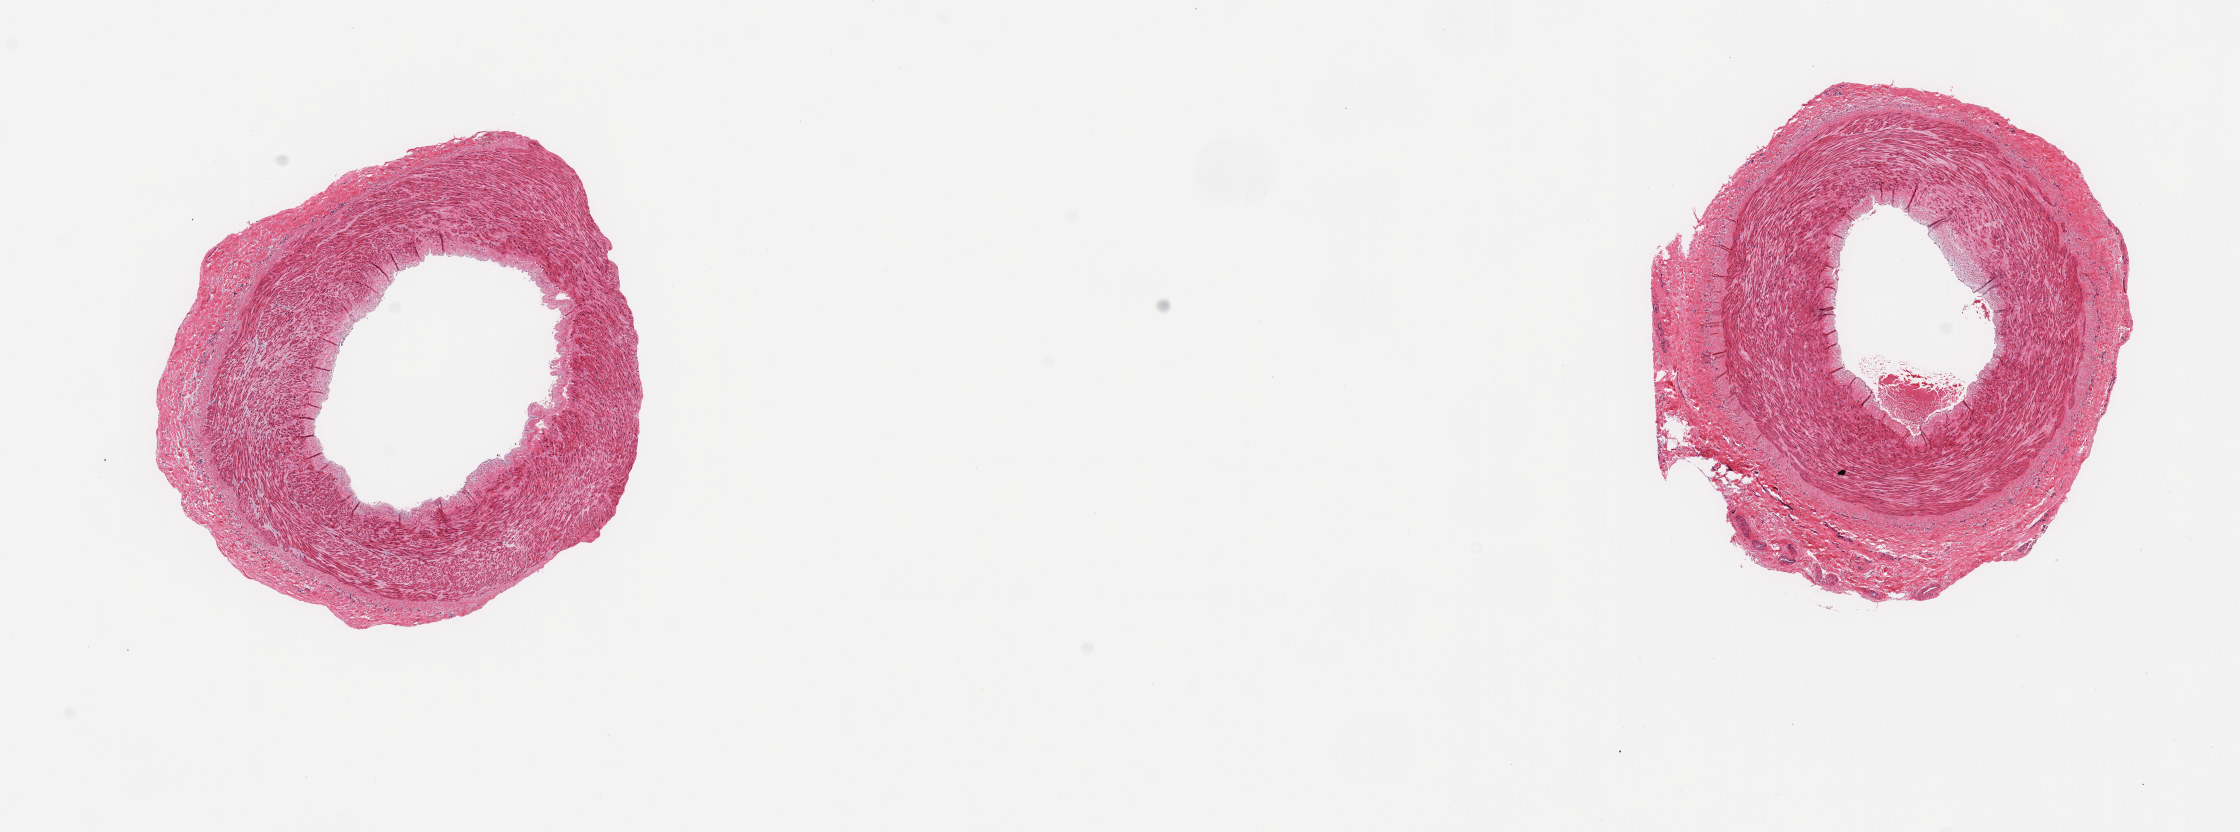
Digitized haematoxylin and eosin-stained section, low-resolution overview of the scanned area, about 17.7 x 6.6 mm. PAXgene-fixed paraffin-embedded (PFPE) section. Sampled site (target tissue): tibial artery. Tissue donor sample. Female donor.
Pathologist's review note for this sample: 2 pieces; well trimmed.